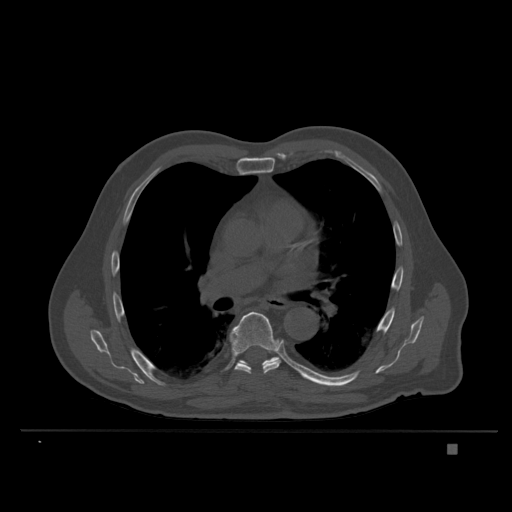
CT including the spine, one axial slice; slice 242 of 435 in the series (ordered by position); bone window (W 1800 / L 400 HU); 512 × 512 image matrix. Patient: male, 73 years. From the clinical record (not read from this slice): primary cancer: skin.
Annotated regions visible in this slice (semi-automatic segmentation, software-assisted and operator-edited):
- T7 vertebra: box from (x=230, y=311) to (x=281, y=374) px
- T8 vertebra: (x=238, y=357)–(x=280, y=367)